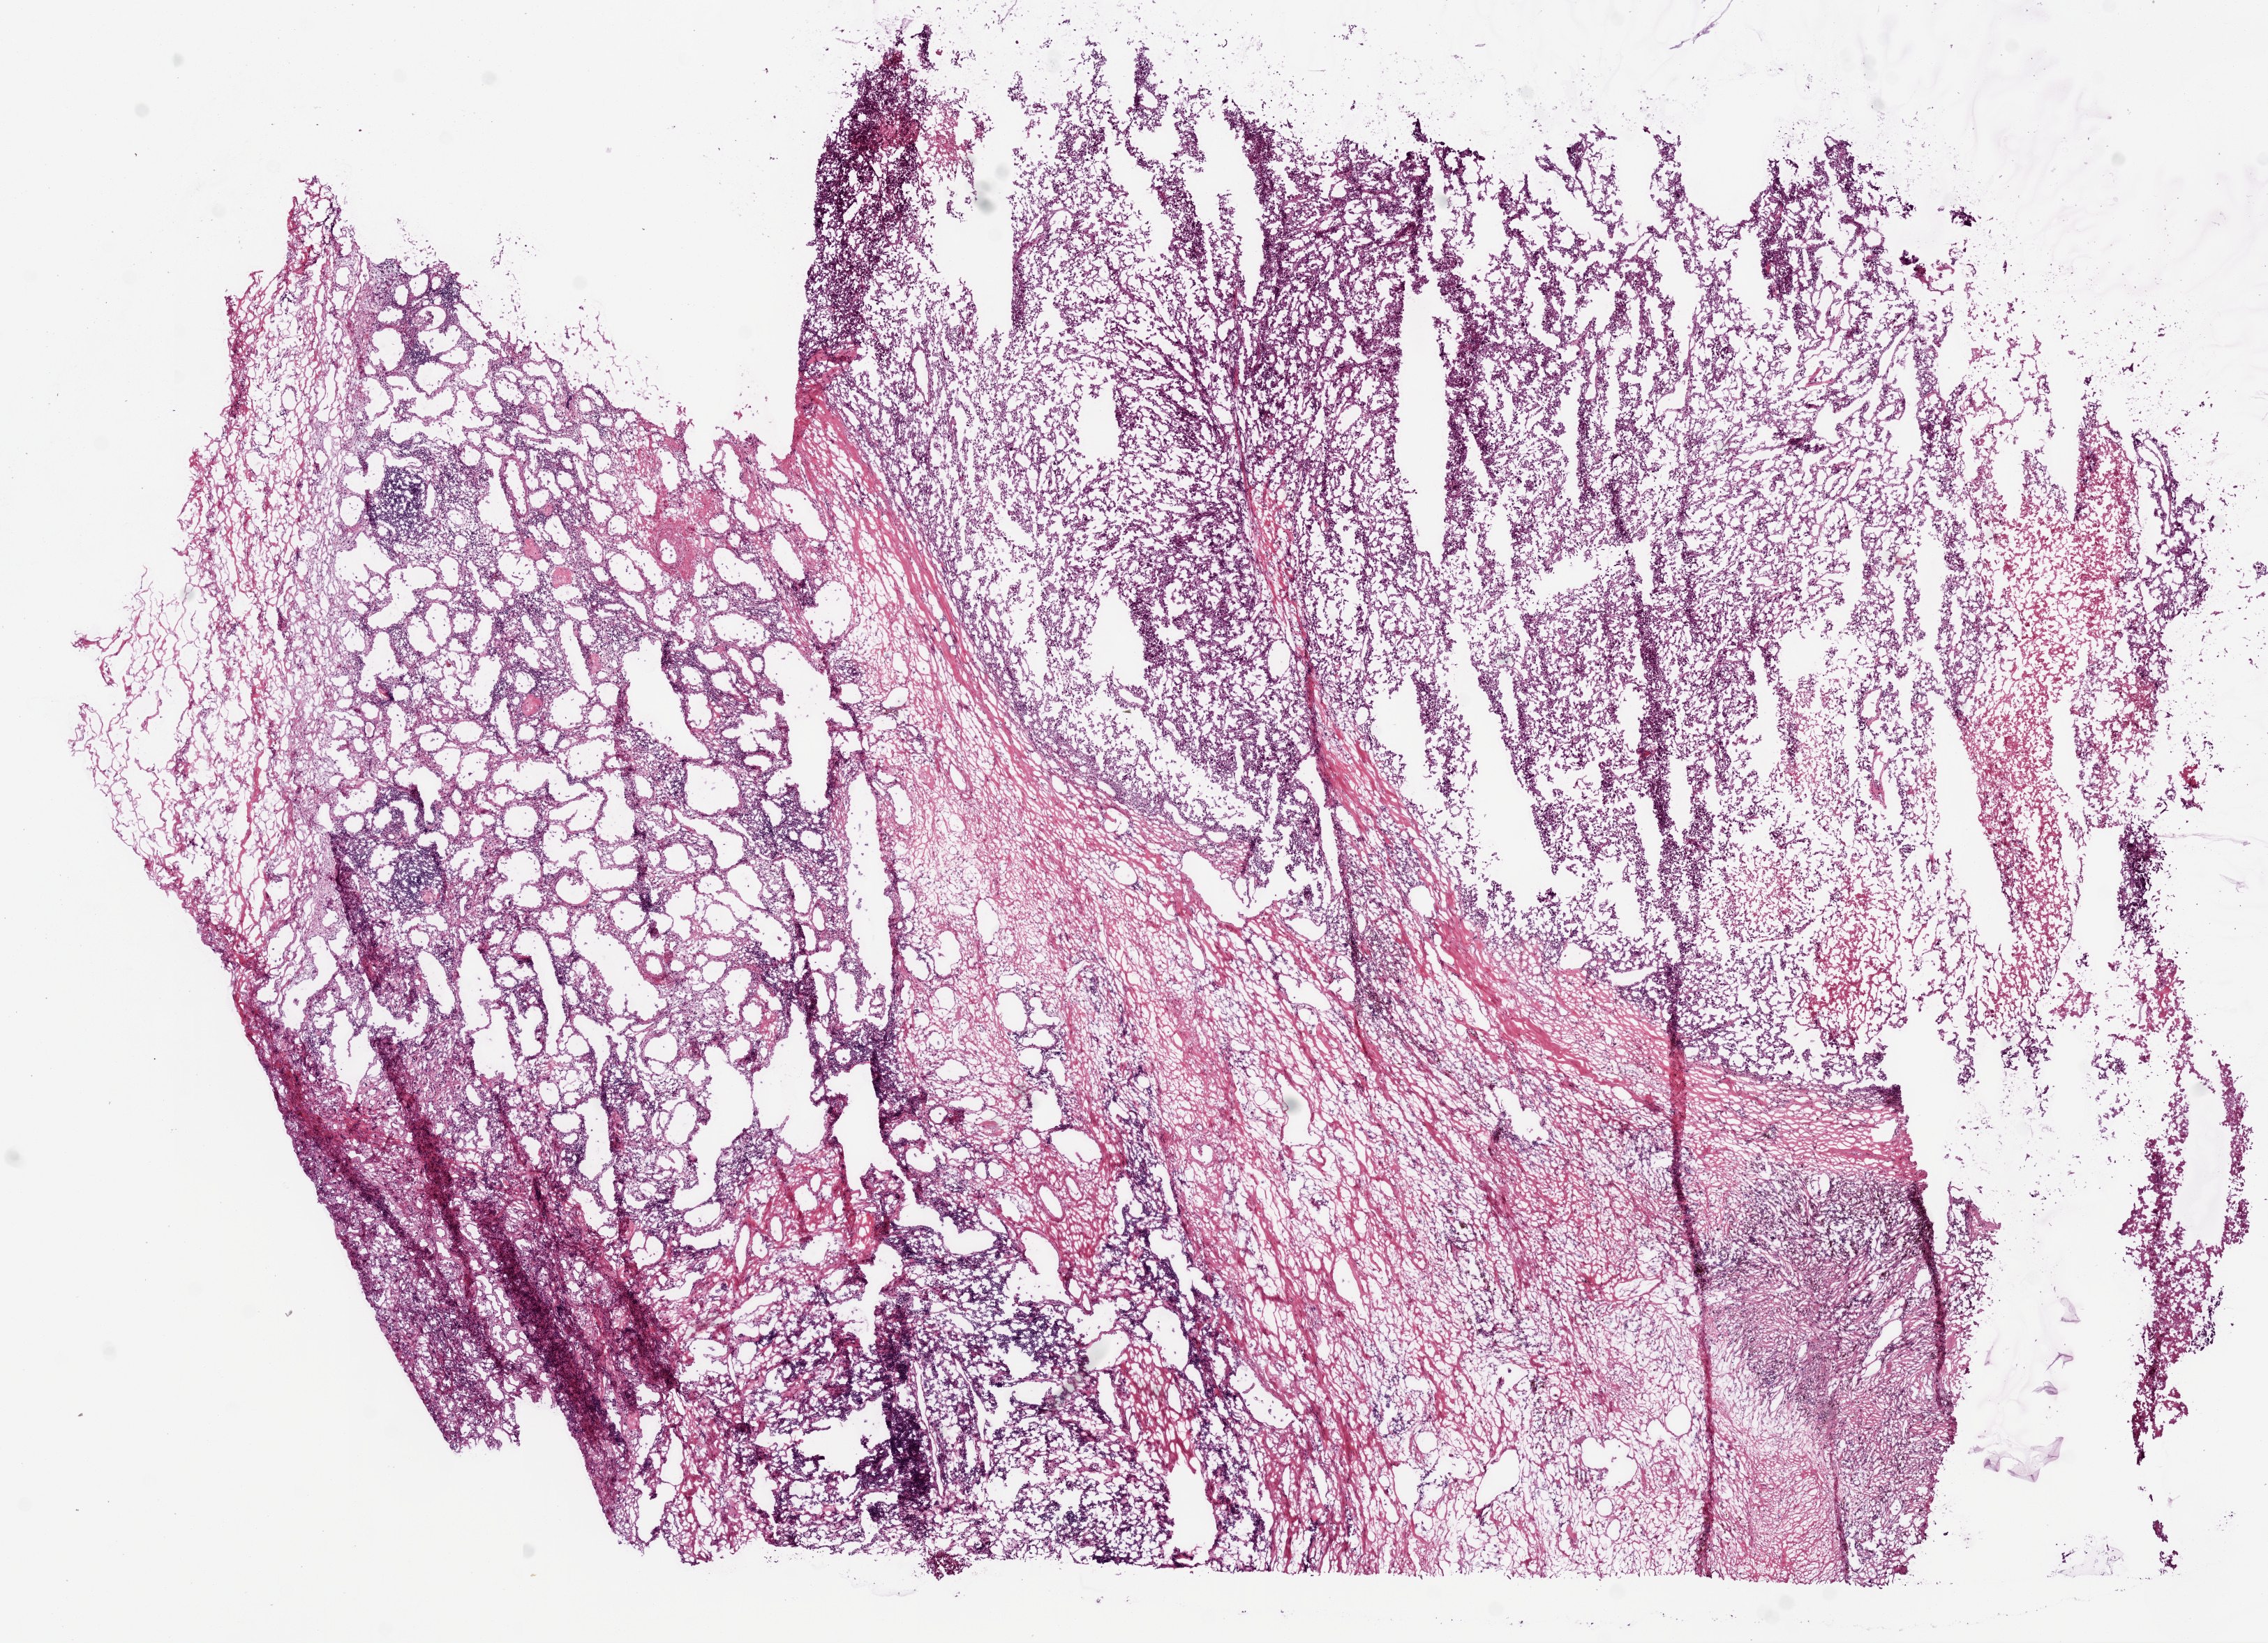
Whole-slide histology image, H&E-stained — low-resolution overview of the scanned area, about 13.0 x 9.4 mm; frozen section; primary tumour sample from the kidney. Patient: female, age at initial diagnosis 60 years. Histologic grade: G4 (undifferentiated). Composition of this section per pathologist review: tumour cells 90%, tumour nuclei 85%, normal cells 0%, stromal cells 10%, necrosis 0%.
AJCC pathologic stage: IV. TNM: T3b NX M1. Pathologic diagnosis: Clear cell adenocarcinoma, NOS.